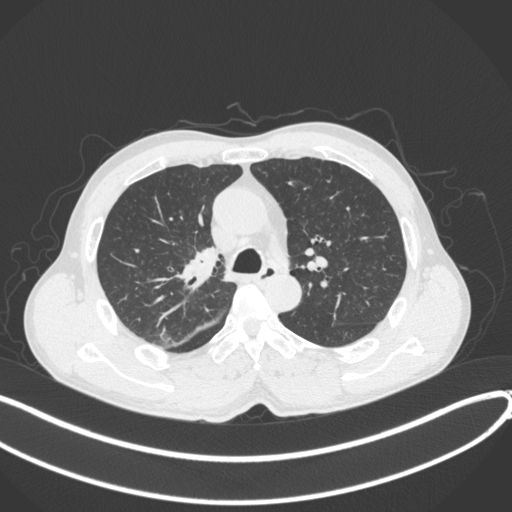
Chest CT, one axial slice; position 263 of 409 along the scan axis; reconstruction kernel B31f; 120 kVp; lung window (W 1500 / L -600 HU); 1 mm slice thickness; 512 × 512 image matrix. Patient: male, 53 years. Case-level facts recorded for this patient, not image findings: clinical TNM (as recorded): T1b N0 M0.
Outlined on this slice (rectangle marked by the reading radiologist):
- lung tumour (recorded histology: squamous cell carcinoma): bounding box <171,243,226,293> (left, top, right, bottom; pixels)